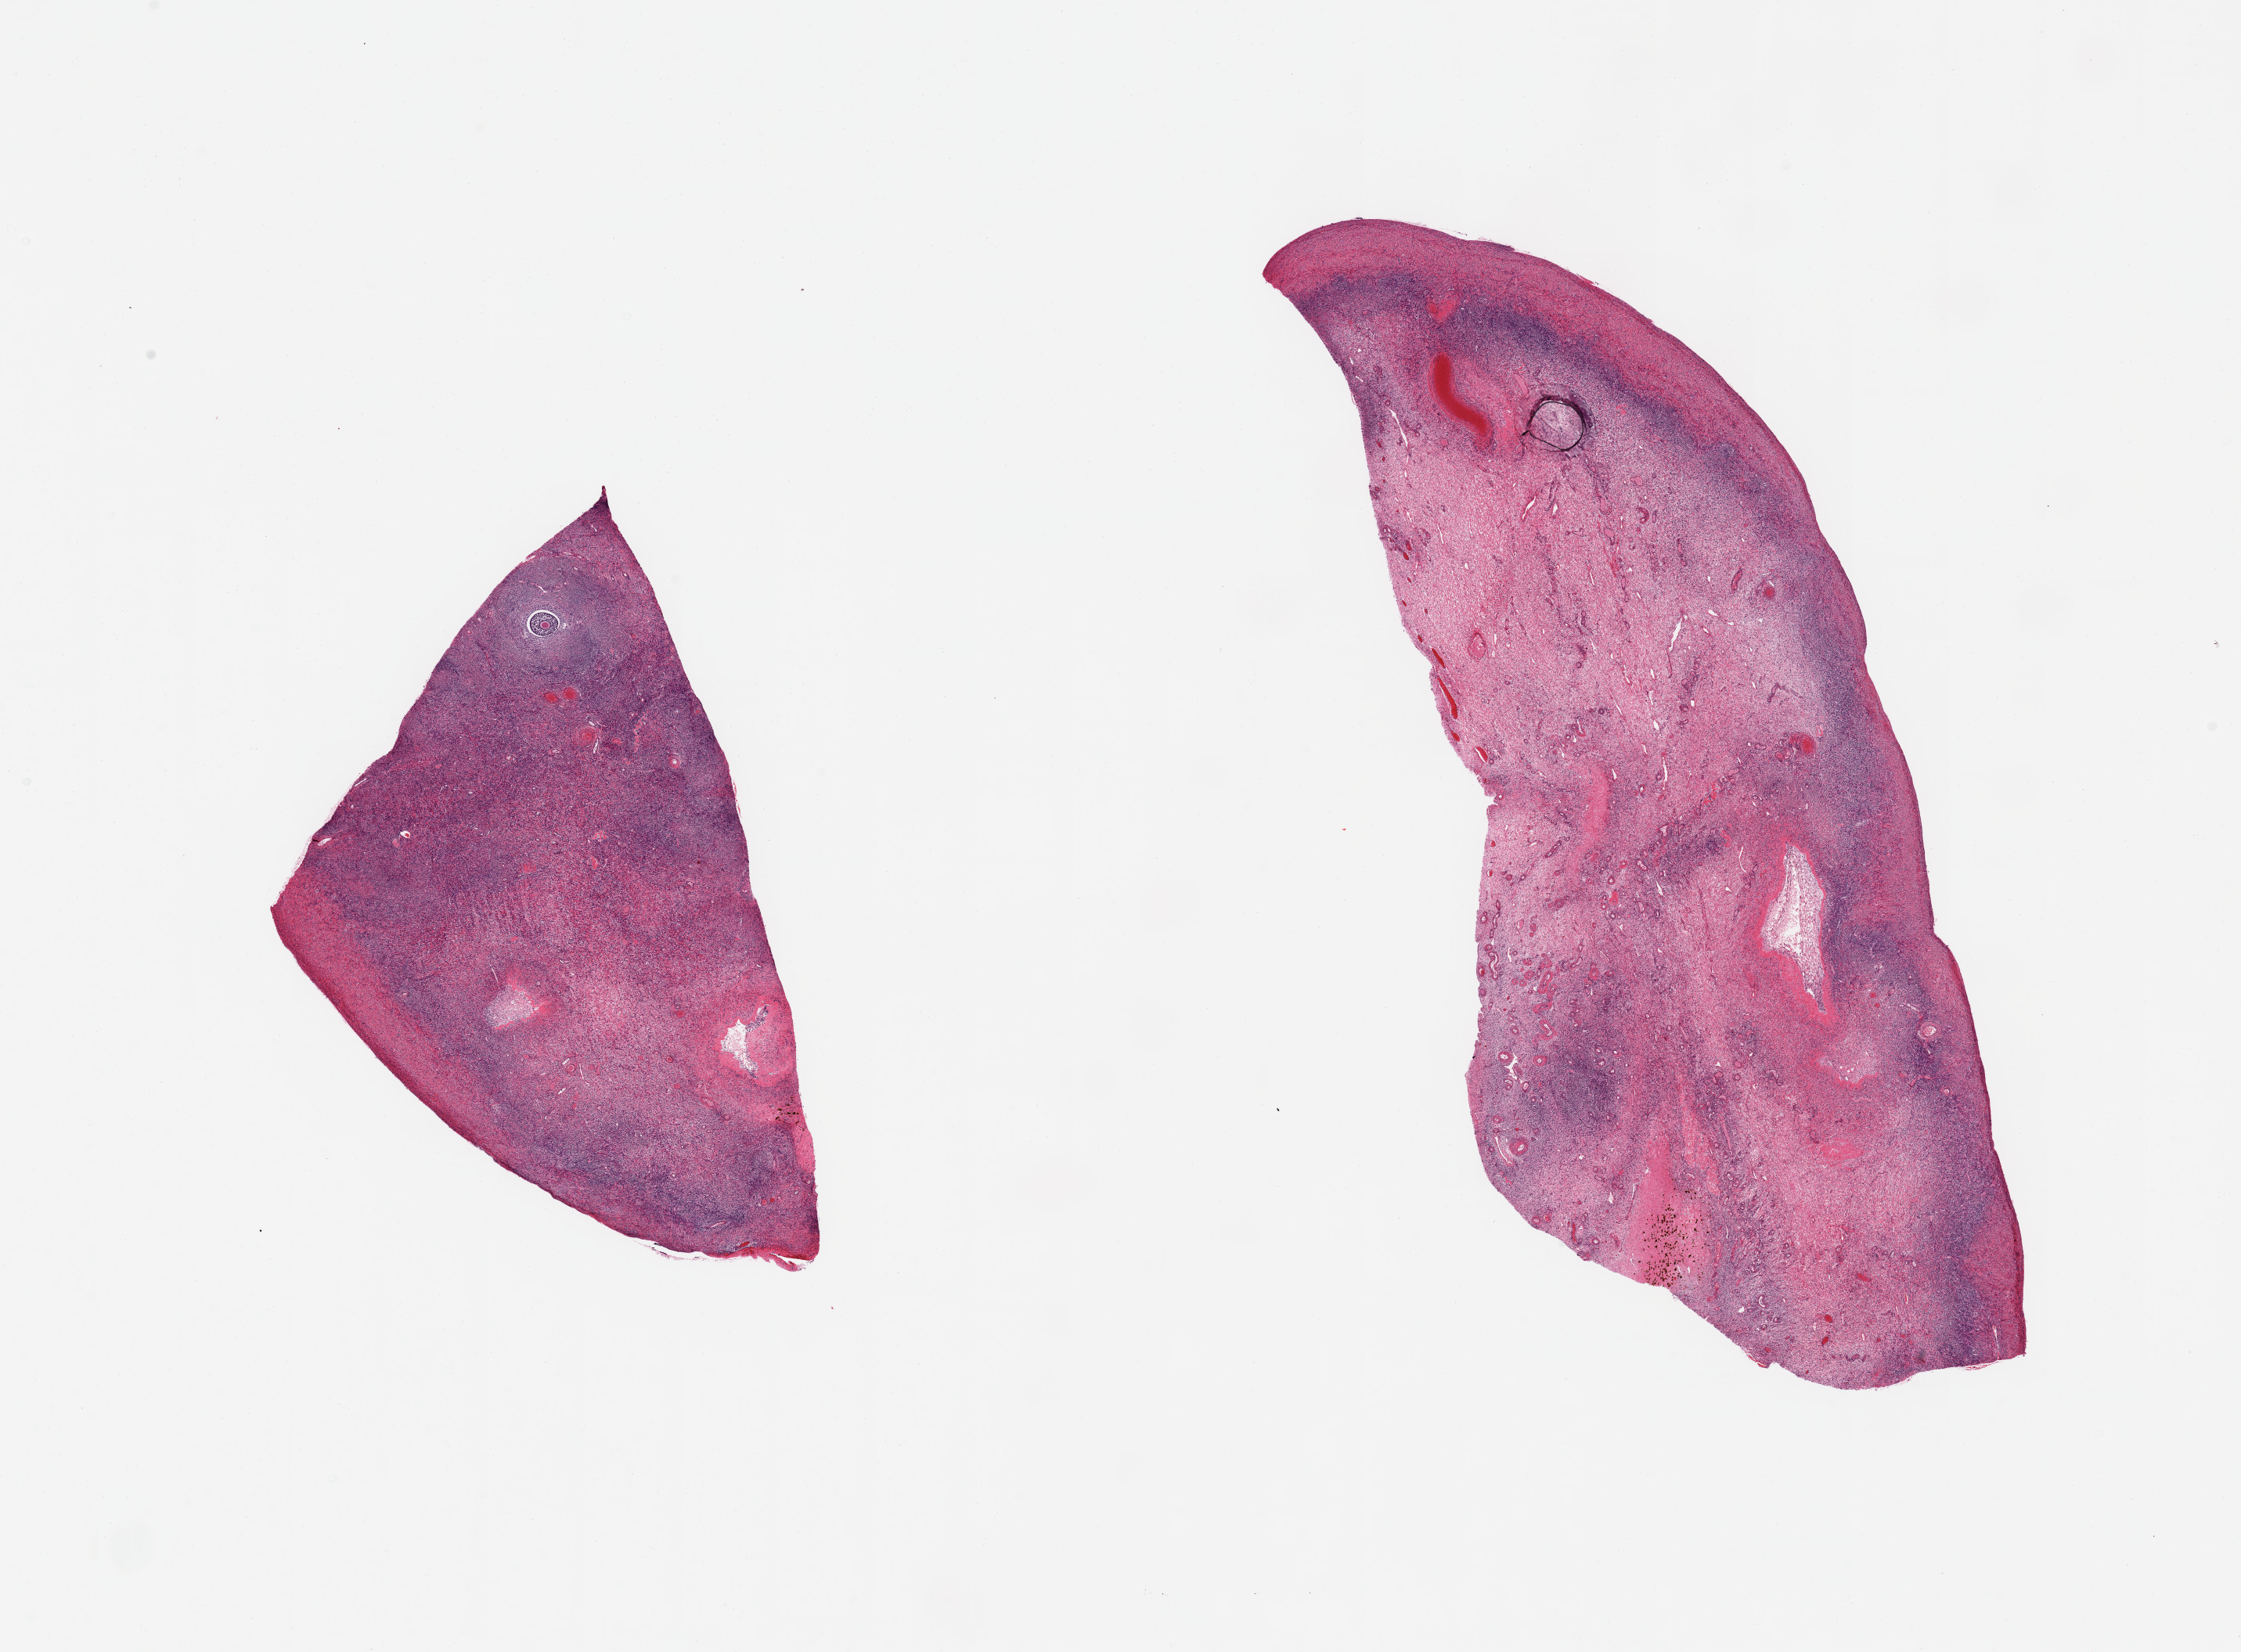
Haematoxylin and eosin whole-slide image — low-resolution overview of the scanned area, about 22.6 x 16.7 mm, PAXgene-fixed paraffin-embedded (PFPE) section, target tissue: ovary, donor tissue sample. Donor: female.
Review note (as recorded): 2 pieces; ovum present.